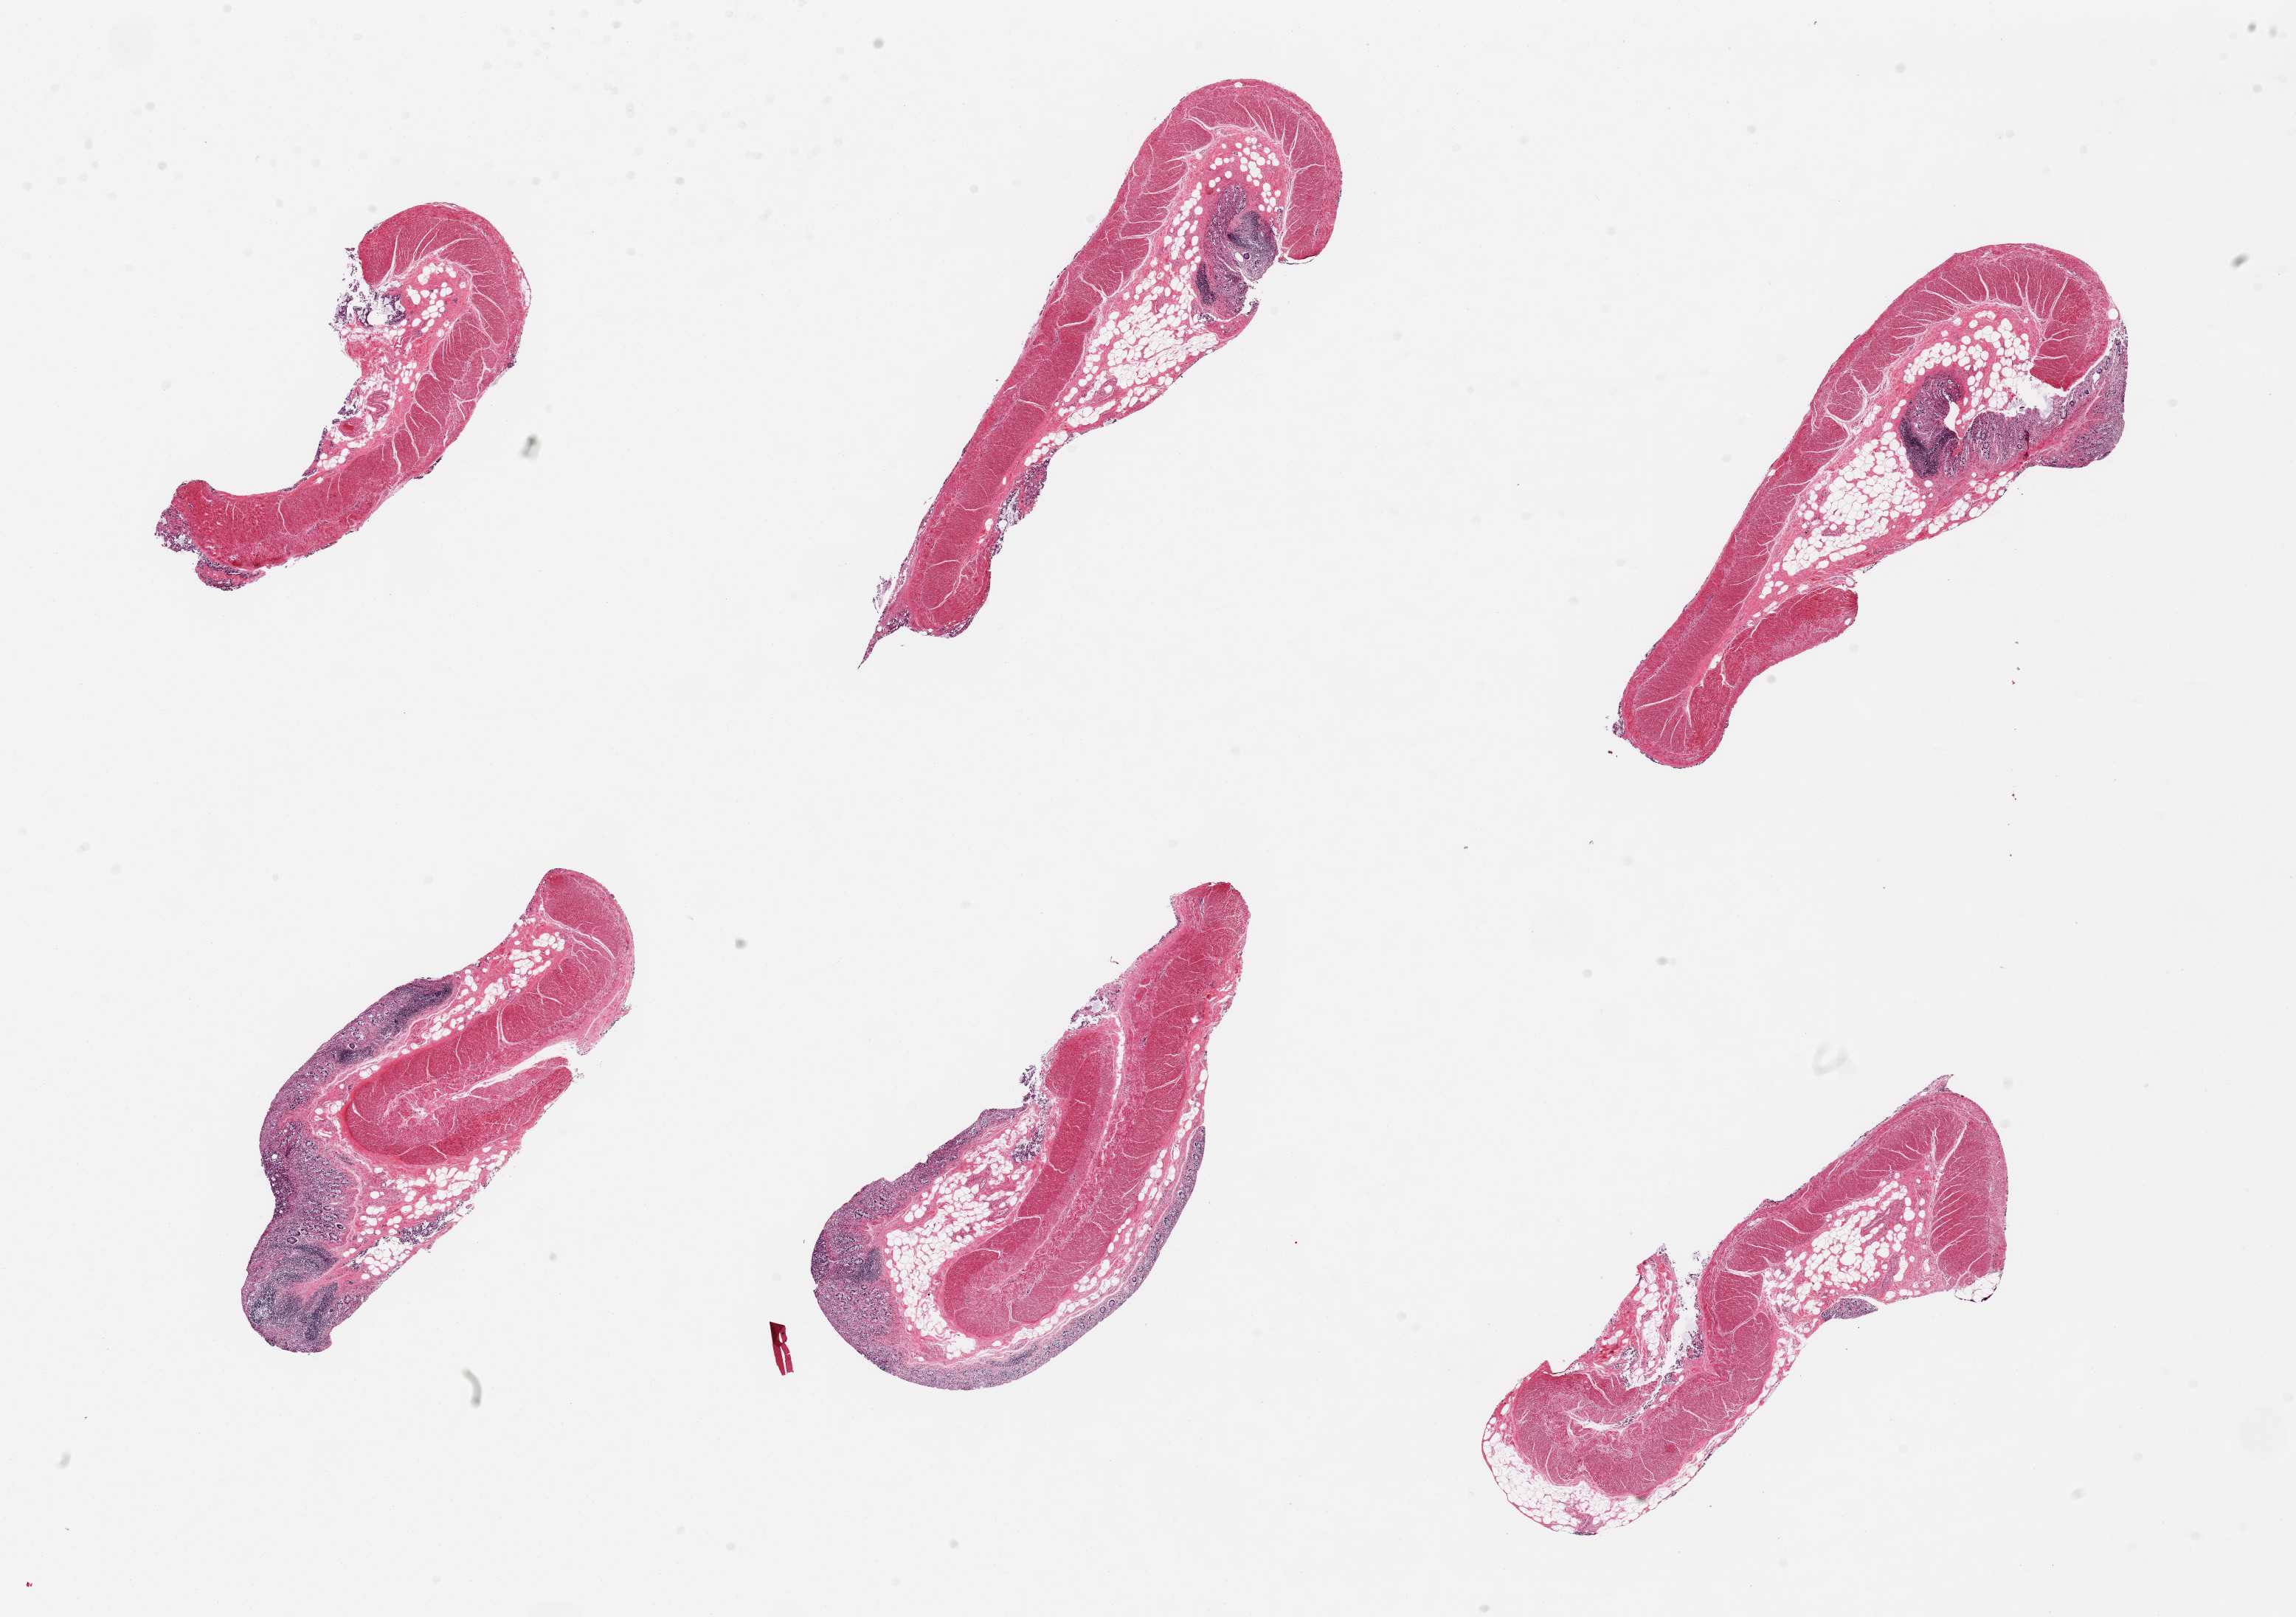
Whole-slide image, haematoxylin and eosin stain — low-resolution overview of the scanned area, about 24.6 x 17.3 mm.
Specimen: PAXgene-fixed, paraffin-embedded tissue; target tissue: transverse colon; donor tissue sample.